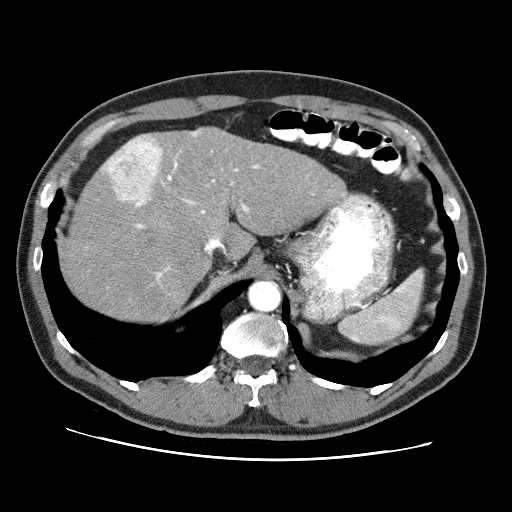
Contrast-enhanced abdominal CT (liver protocol), one axial slice; slice 53 of 71 in the series (ordered by position); reconstruction kernel STANDARD; 120 kVp; soft-tissue window (W 400 / L 40 HU); 2.5 mm slice thickness; 512 × 512 image matrix, field of view 360 × 360 mm. Case-level facts recorded for this patient, not image findings: diagnosis: hepatocellular carcinoma (patient treated with transarterial chemoembolisation; whether this scan precedes or follows treatment is not stated here); TNM stage (as recorded): Stage-II; Child-Pugh class: A.
Outlined on this slice (semi-automatic segmentation, software-assisted and operator-edited):
- abdominal aorta: bounding box [x1, y1, x2, y2] px = [249, 281, 280, 311]
- liver parenchyma outside the tumour (the mass and vessels are separate outlines, so this box may not span the whole liver): [62, 126, 346, 322]
- mass: [109, 138, 161, 204]
- liver vessels: [106, 132, 259, 279]